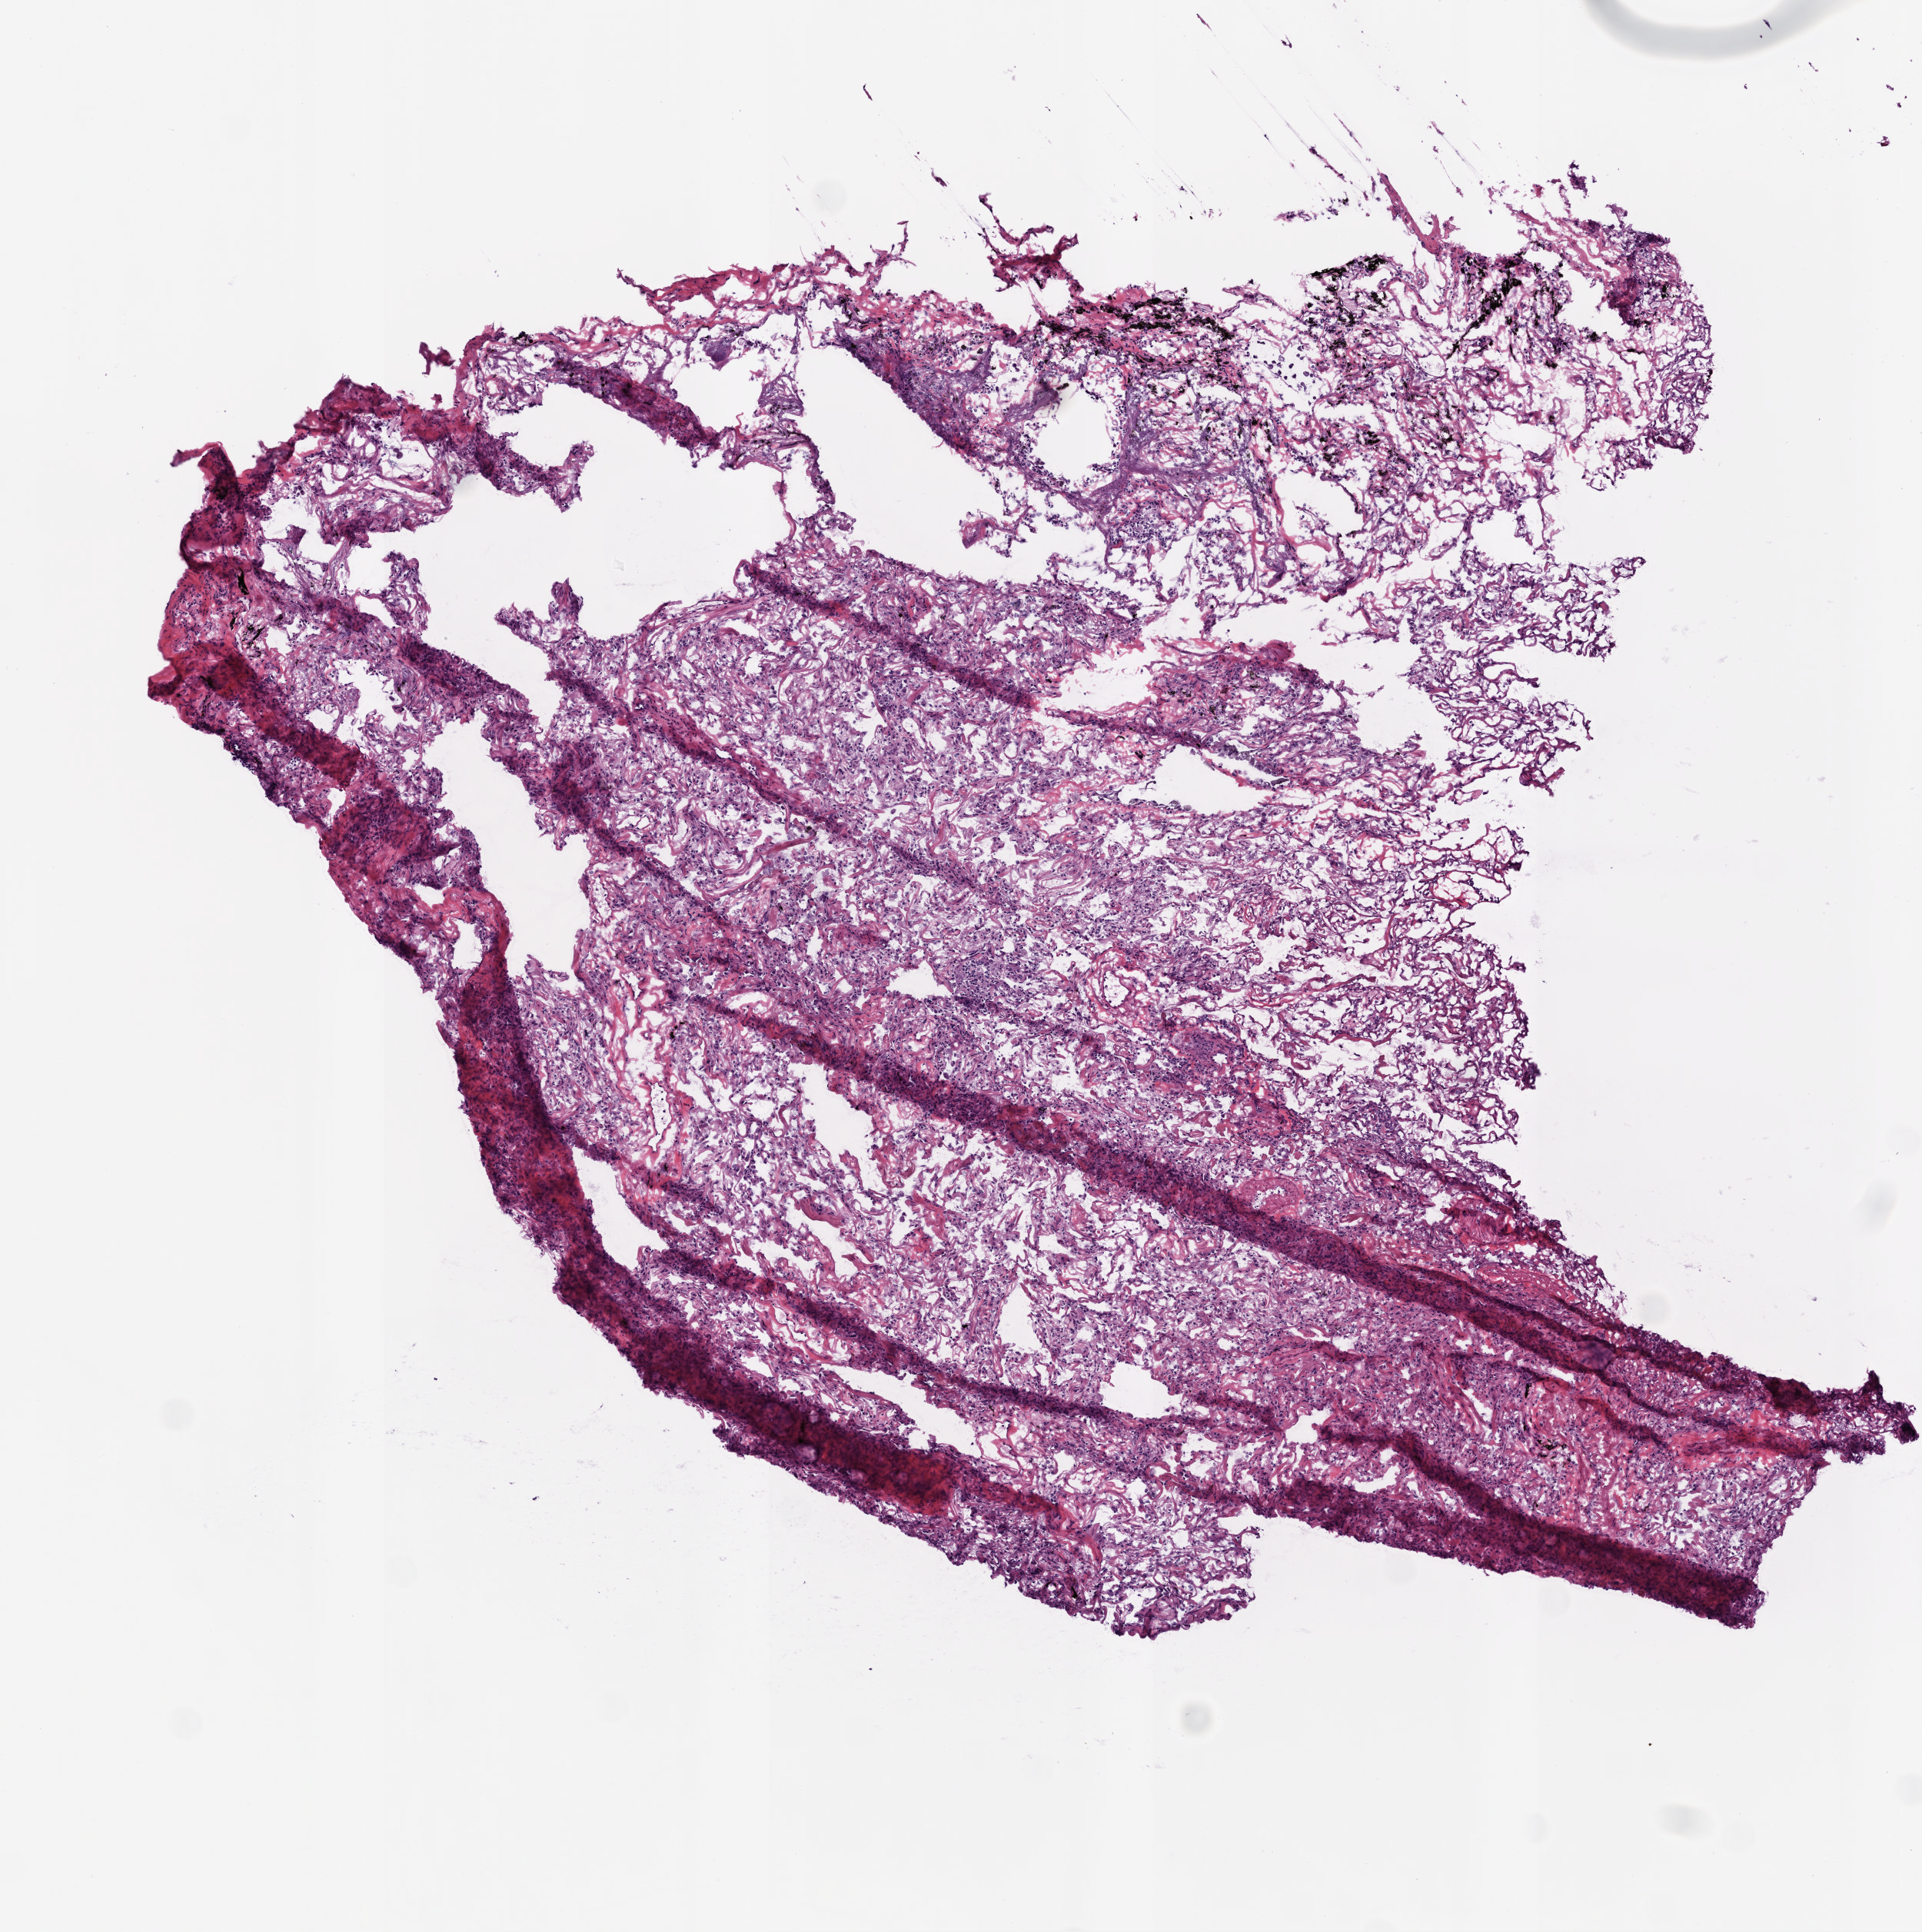
Digitized H&E-stained tissue section (whole slide), whole scanned area (about 5.0 x 5.0 mm, acquisition: 20x scan) shown as a low-resolution overview, frozen section, sample: solid tissue normal (non-tumour tissue), lung. Male, age 70 years at initial diagnosis.
This section: solid tissue normal (non-tumour) sample from the same patient. Patient diagnosis: Squamous cell carcinoma, NOS (upper lobe, lung).